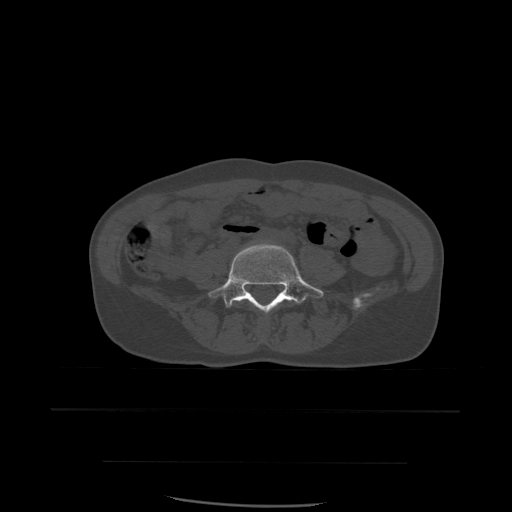
CT including the spine, one axial slice. Slice 154 of 574 in the series (ordered by position). Bone window (W 1800 / L 400 HU). 512 × 512 image matrix, field of view 392 × 392 mm. Patient age 48 years. From the clinical record (not read from this slice): primary cancer: lung.
Annotated regions visible in this slice (semi-automatic segmentation, software-assisted and operator-edited):
- L4 vertebra: bounding box (x1, y1, x2, y2) in pixels: (238, 291, 248, 305)
- L5 vertebra: (209, 243, 324, 312)